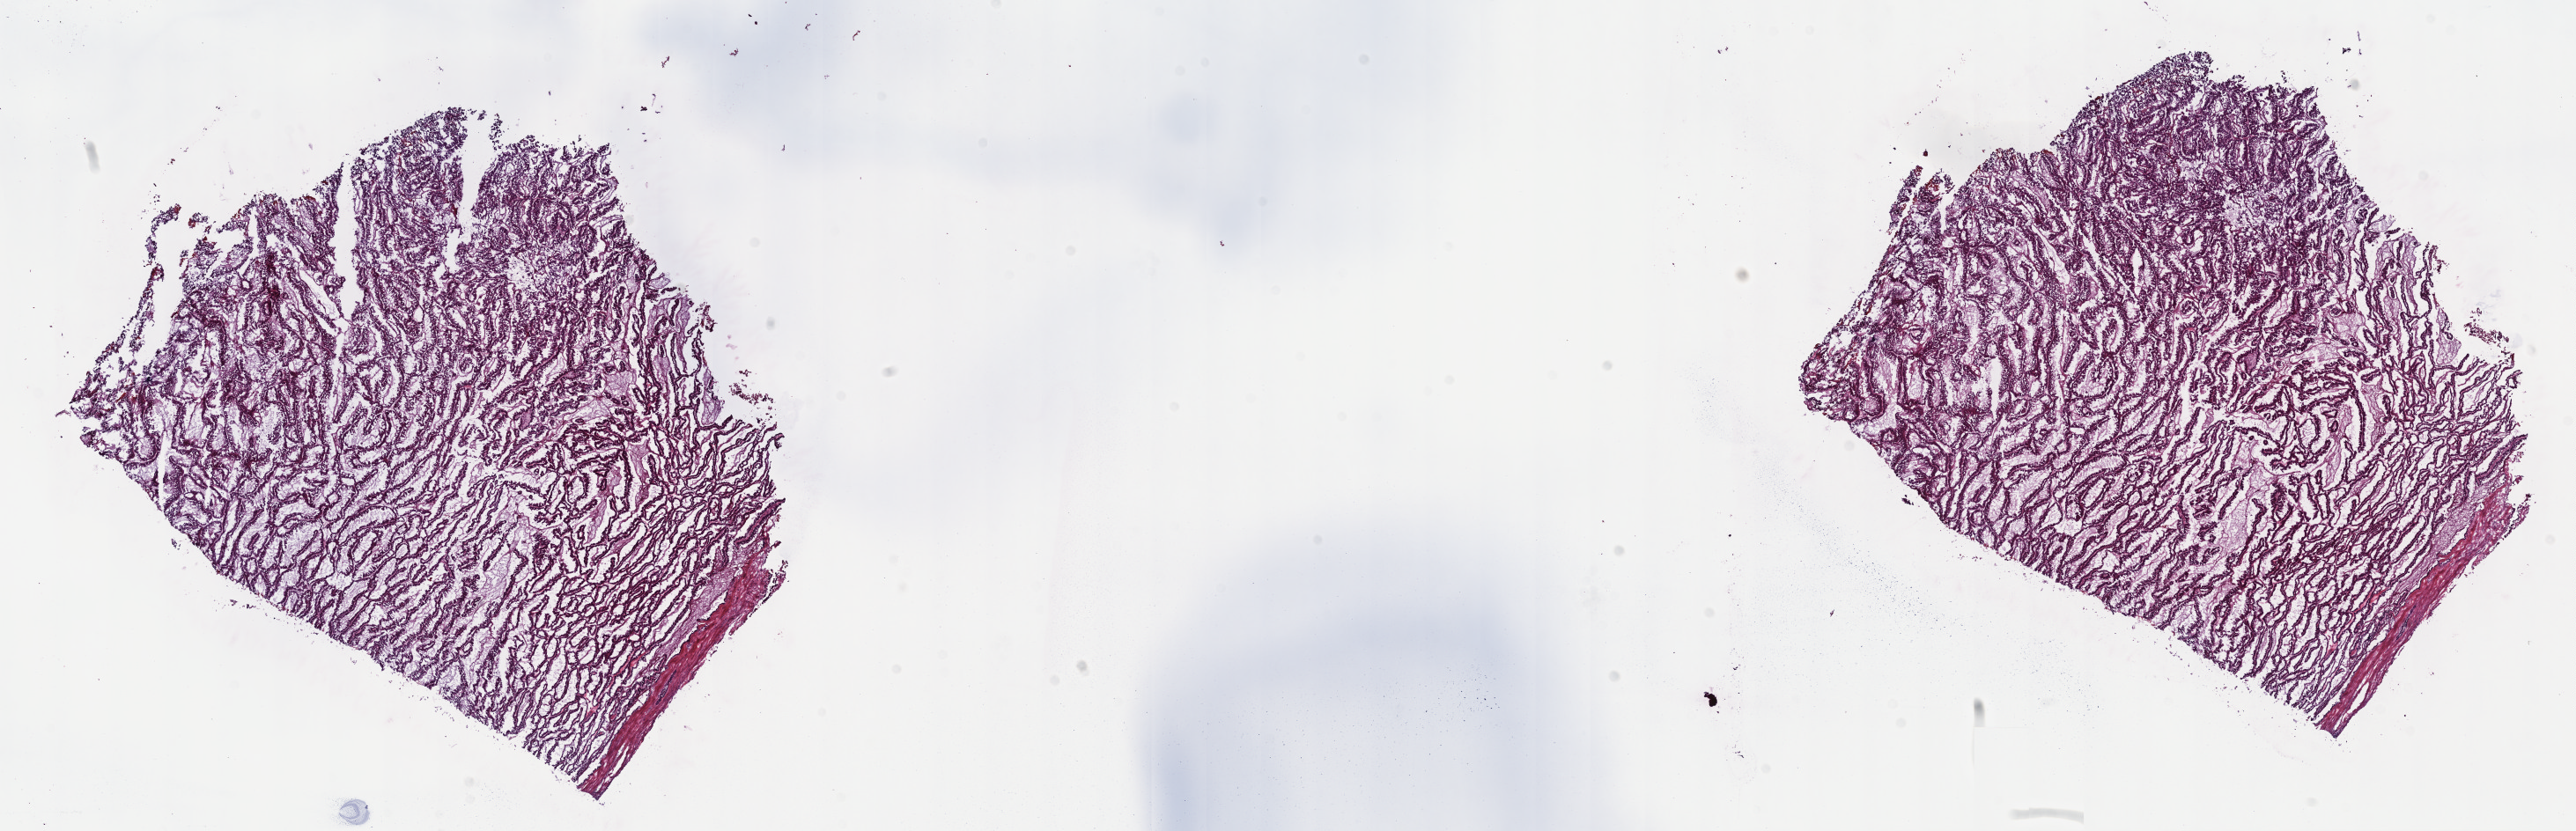
Whole-slide histology image, H&E — a low-resolution overview of the entire scanned area, about 23.7 x 7.6 mm (slide scanned at 40x). Frozen section from the top of the tissue portion. Kidney, primary tumour sample. Male, age 66 years at initial diagnosis. Slide review estimates, as recorded: tumour cells 75%, tumour nuclei 75%, normal cells 0%, stromal cells 25%, necrosis 0%. Inflammatory infiltration, as recorded: lymphocyte infiltration 0%, monocyte infiltration 5%, neutrophil infiltration 0%.
• diagnosis: Papillary adenocarcinoma, NOS
• laterality: right
• AJCC pathologic stage: I (7th edition)